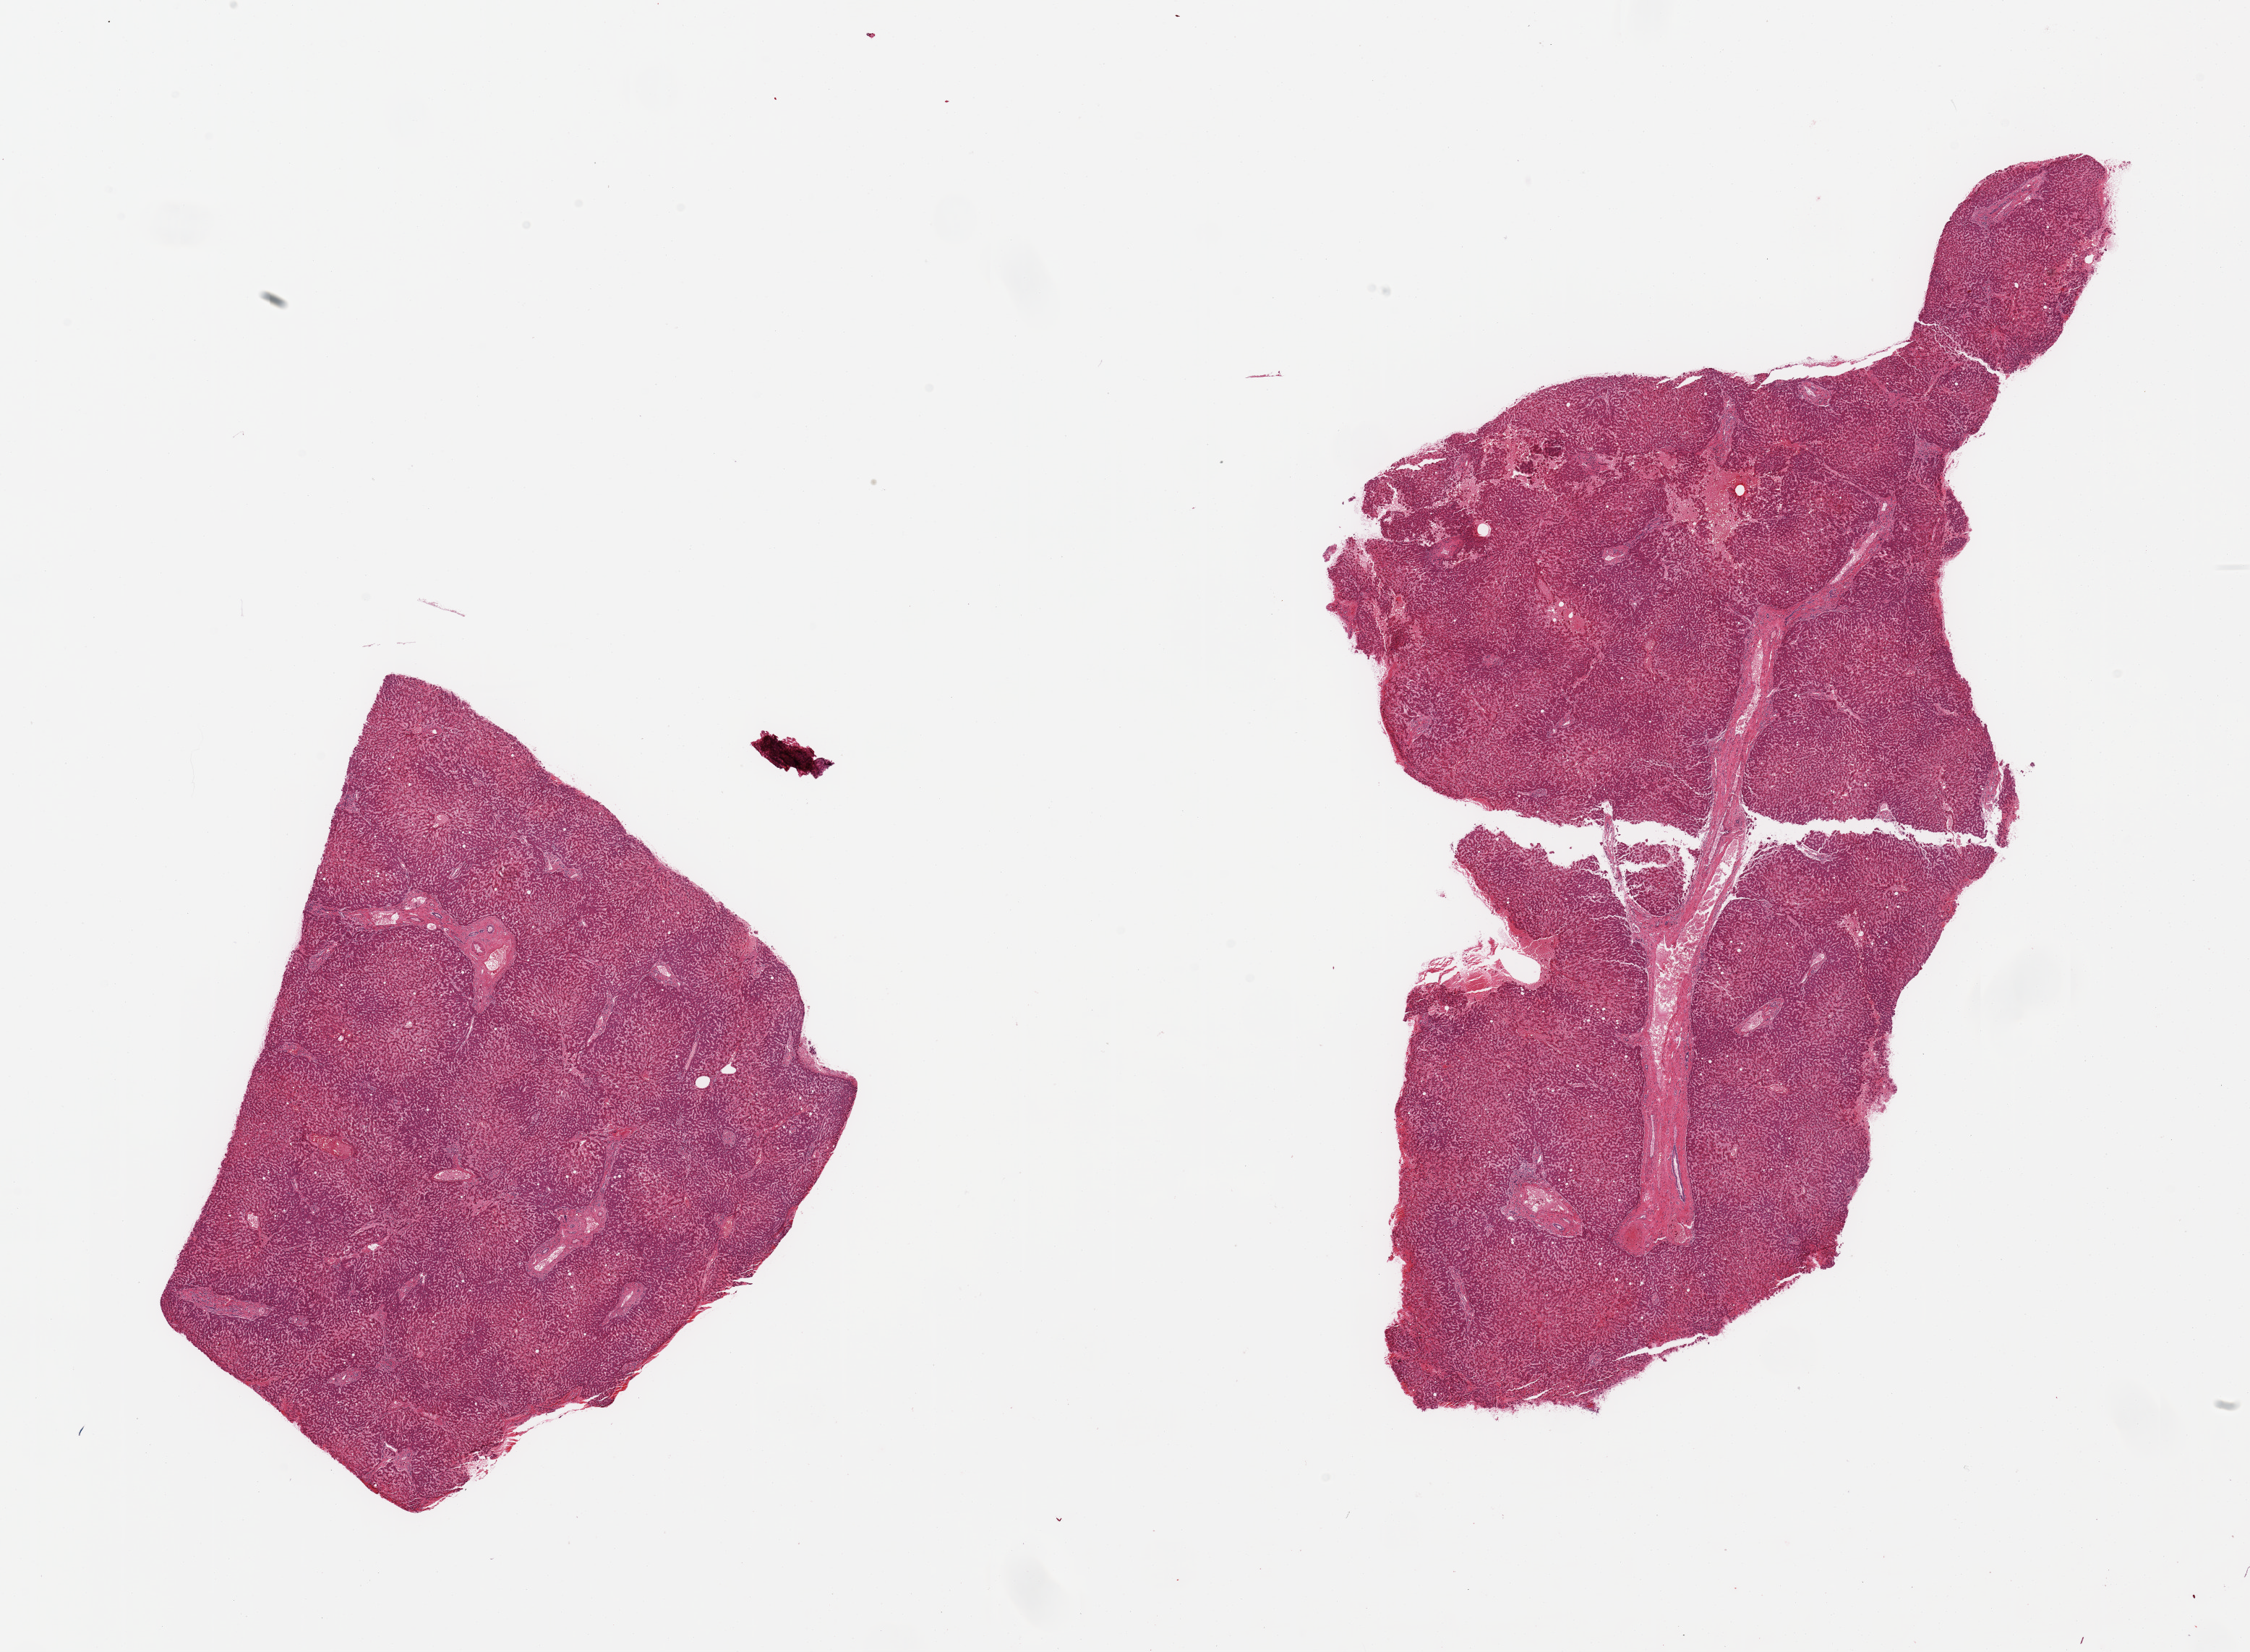
Whole-slide image, hematoxylin and eosin (H&E) stain — low-resolution overview of the scanned area, about 24.6 x 18.1 mm (from a 20x scan). PAXgene-fixed paraffin-embedded (PFPE) section. Section of liver (target tissue). Tissue donor sample. Male donor.
Pathologist's review note for this sample: 2 pieces; moderate centrilobular congestion with mild centrilobular macrovesicular steatosis.